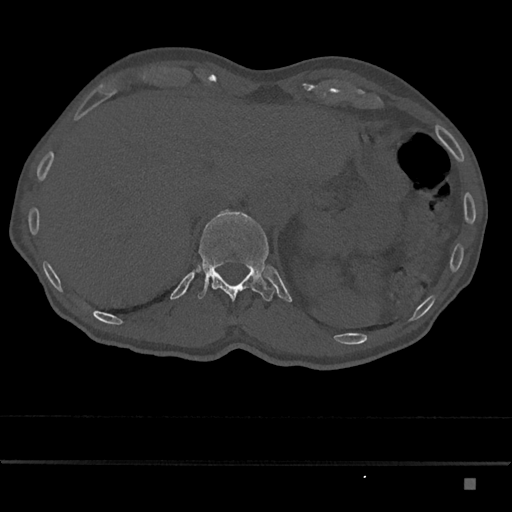
CT including the spine, one axial slice; position 615 of 797 along the scan axis; reconstruction kernel Br40s/3; 120 kVp; bone window (W 1800 / L 400 HU); 512 × 512 image matrix, field of view 390 × 390 mm. Male patient, age 72 years. Case-level facts recorded for this patient, not image findings: primary cancer: prostate.
Annotated regions visible in this slice (semi-automatic segmentation, software-assisted and operator-edited):
- T12 vertebra: bounding box [x1, y1, x2, y2] px = [197, 211, 275, 301]